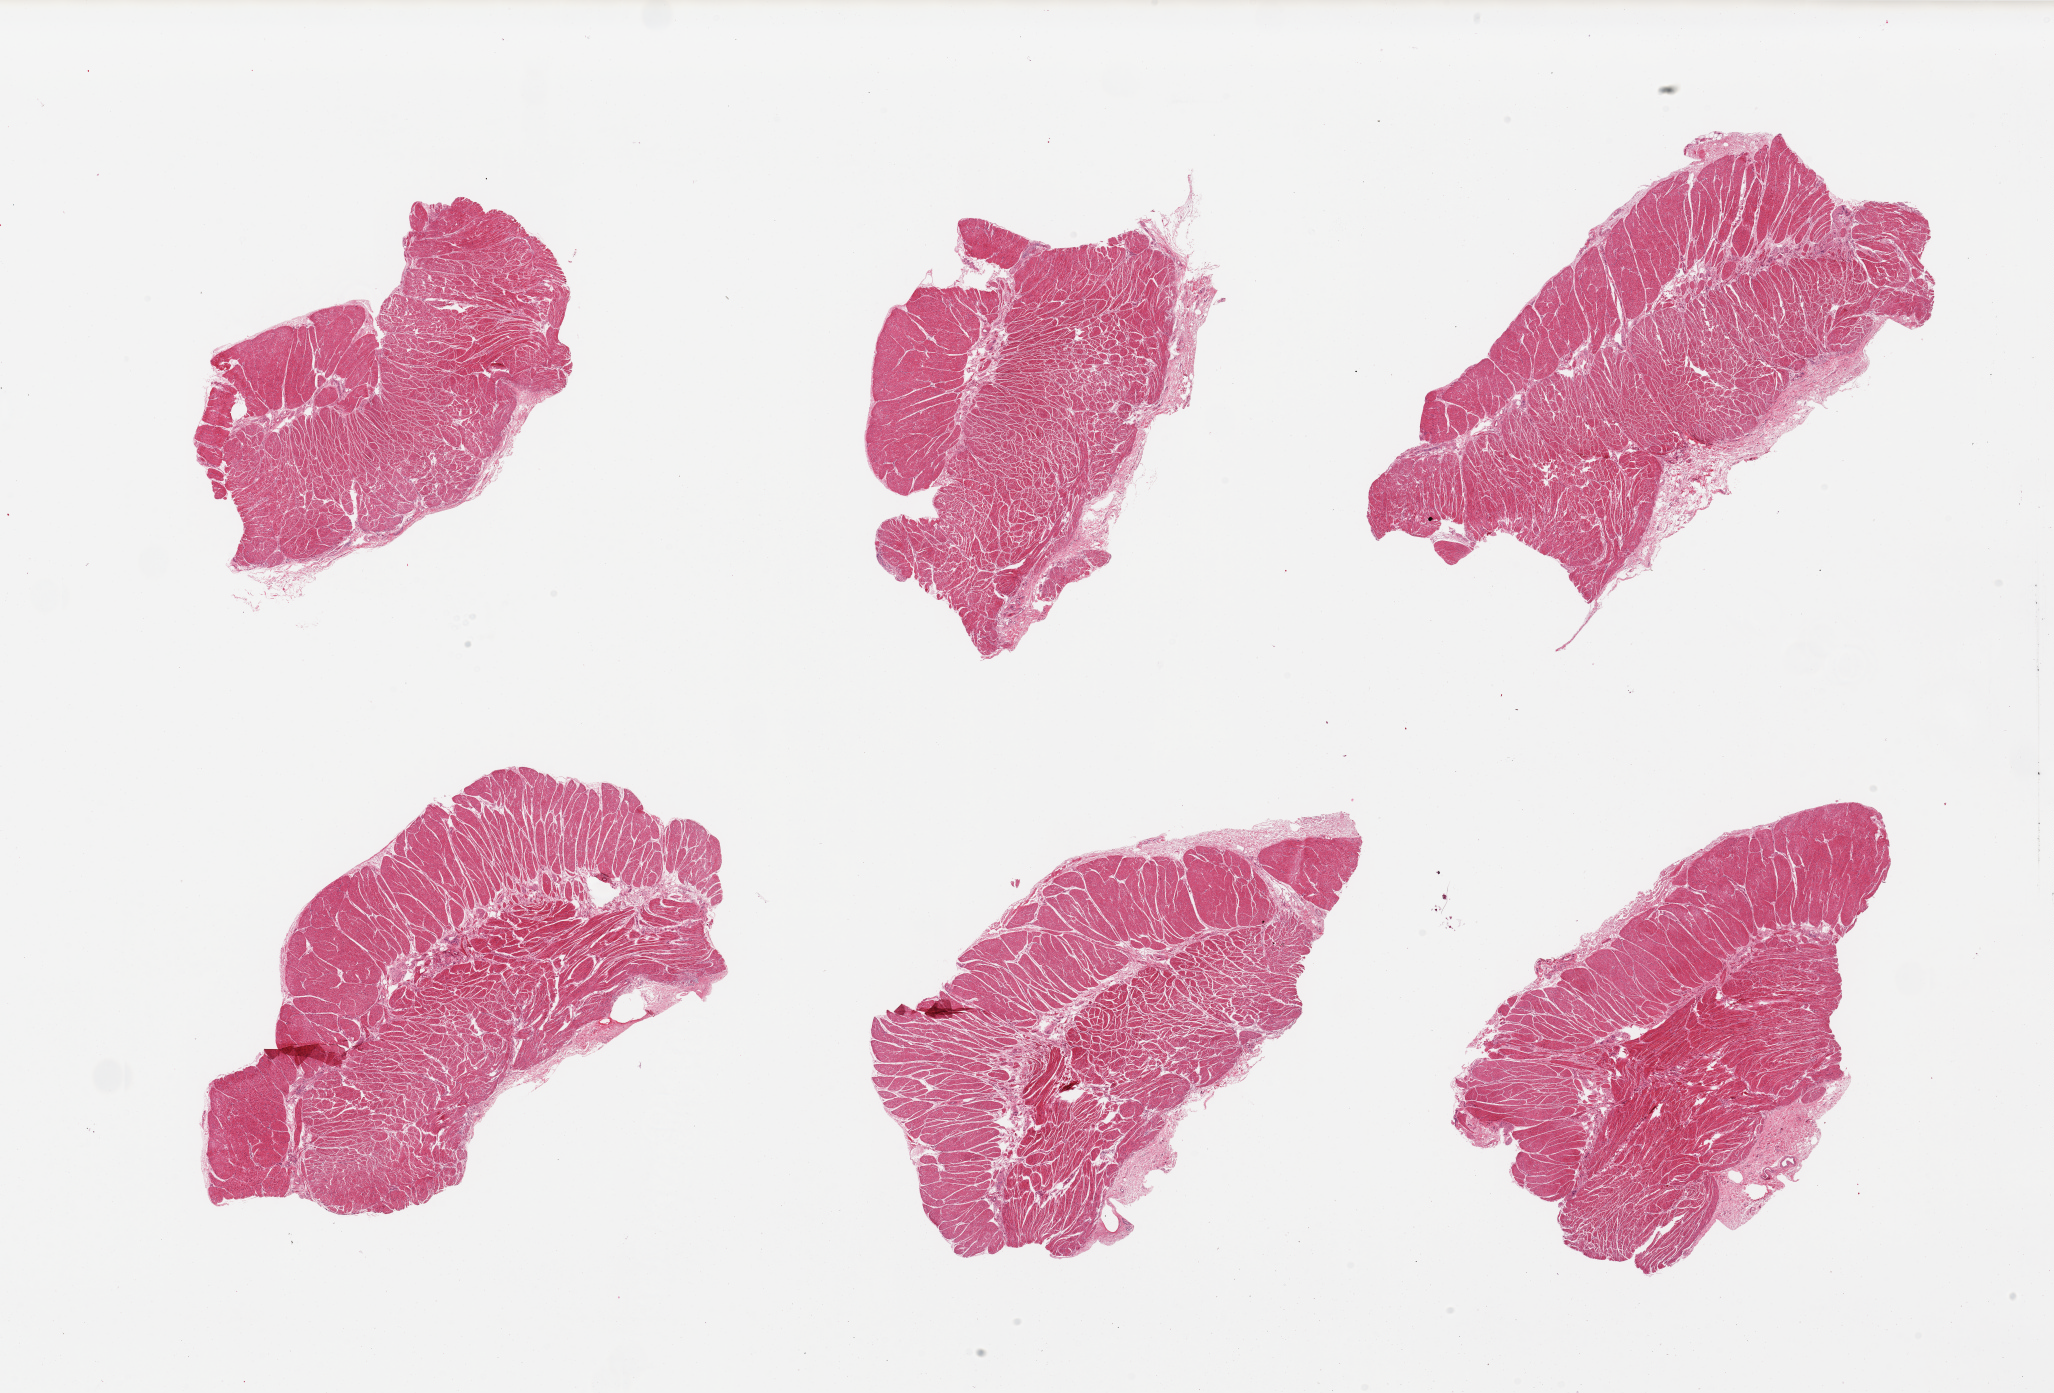
Digitized haematoxylin and eosin-stained section, brightfield, a low-resolution overview of the entire scanned area, about 32.5 x 22.0 mm; PAXgene-fixed, paraffin-embedded tissue; sampled site (target tissue): esophageal muscle; tissue donor sample. Female donor.
Review note (as recorded): 6 pieces. Well dissected.